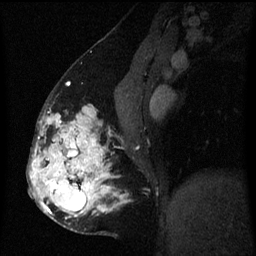
Breast MRI (dynamic contrast-enhanced), one sagittal slice. Position 29 of 60 along the scan axis. Dynamic contrast-enhanced series, image 2 of 3 at this slice position (ordered by acquisition). 1.5 T. TE 4.2 ms, TR 8 ms. 2 mm slice thickness. 256 × 256 image matrix, field of view 190 × 190 mm. Female patient, age 50 years.
Outlined on this slice (semi-automatic segmentation, software-assisted and operator-edited):
- analysis volume of interest (the breast-tissue region the enhancement analysis was run in; not a lesion): bounding box [x1, y1, x2, y2] px = [32, 107, 127, 232]
- tumour enhancement mask (voxels above the 70 % enhancement threshold inside the analysis volume of interest): [32, 107, 127, 219]